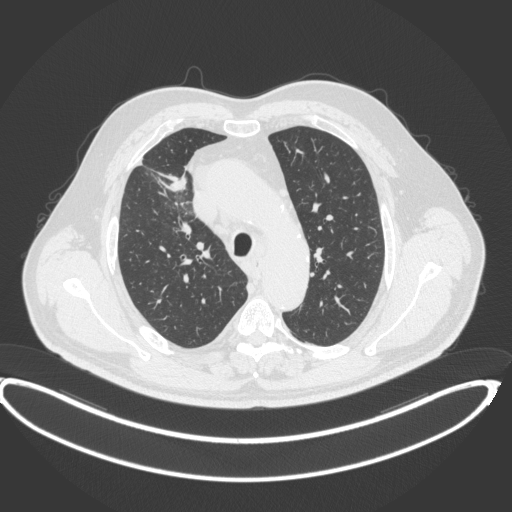
Chest CT, one axial slice. Slice 303 of 395 in the series (ordered by position). Reconstruction kernel B31f. Lung window (W 1500 / L -600 HU). 1 mm slice thickness. 512 × 512 image matrix. Patient: male, 62 years. Case-level facts recorded for this patient, not image findings: clinical TNM (as recorded): T1c N3 M1c.
Structures marked on this image (bounding box drawn by a radiologist):
- lung tumour (recorded histology: adenocarcinoma): box from (x=168, y=174) to (x=188, y=194) px